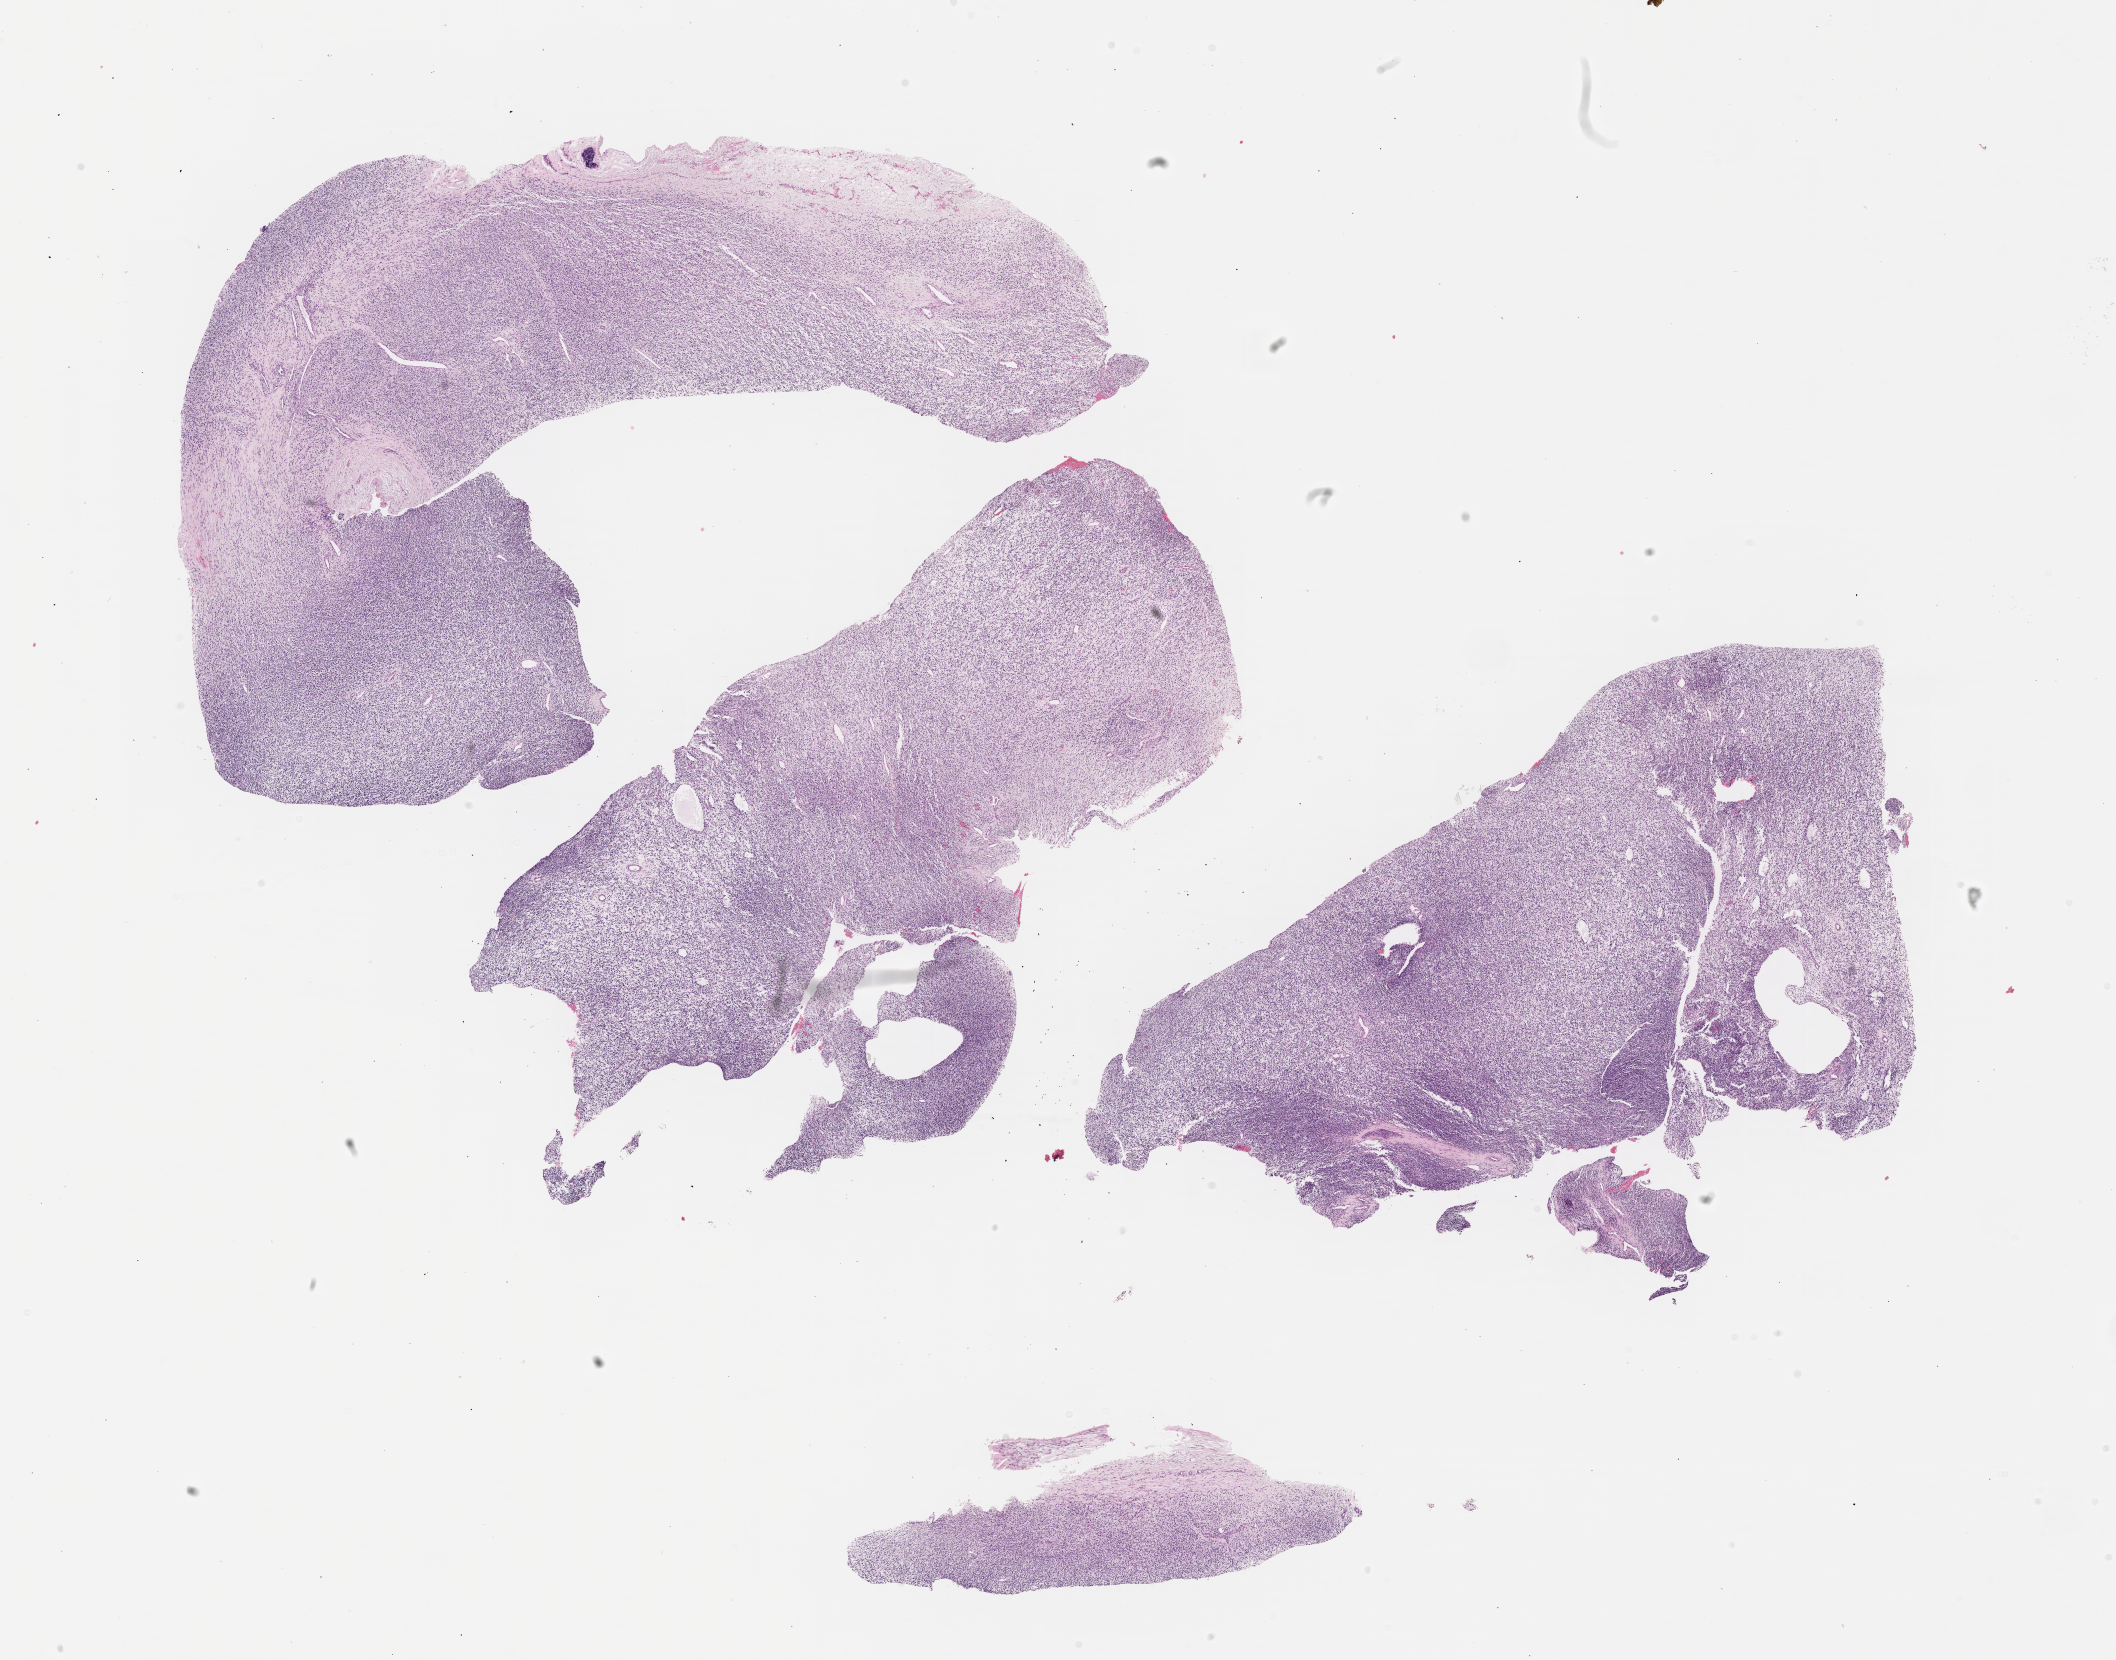
Digitized hematoxylin and eosin (H&E)-stained section of tumor tissue — low-resolution overview of the scanned area, about 17.1 x 13.4 mm, formalin-fixed paraffin-embedded section, sample anatomic site: soft tissue, abdomen. Female patient, age at diagnosis 0.1 years.
Diagnosis: rhabdomyosarcoma; histological classification: embryonal rhabdomyosarcoma. Metastatic status at presentation (as recorded): non-metastatic (confirmed). Stage (as recorded): 3.